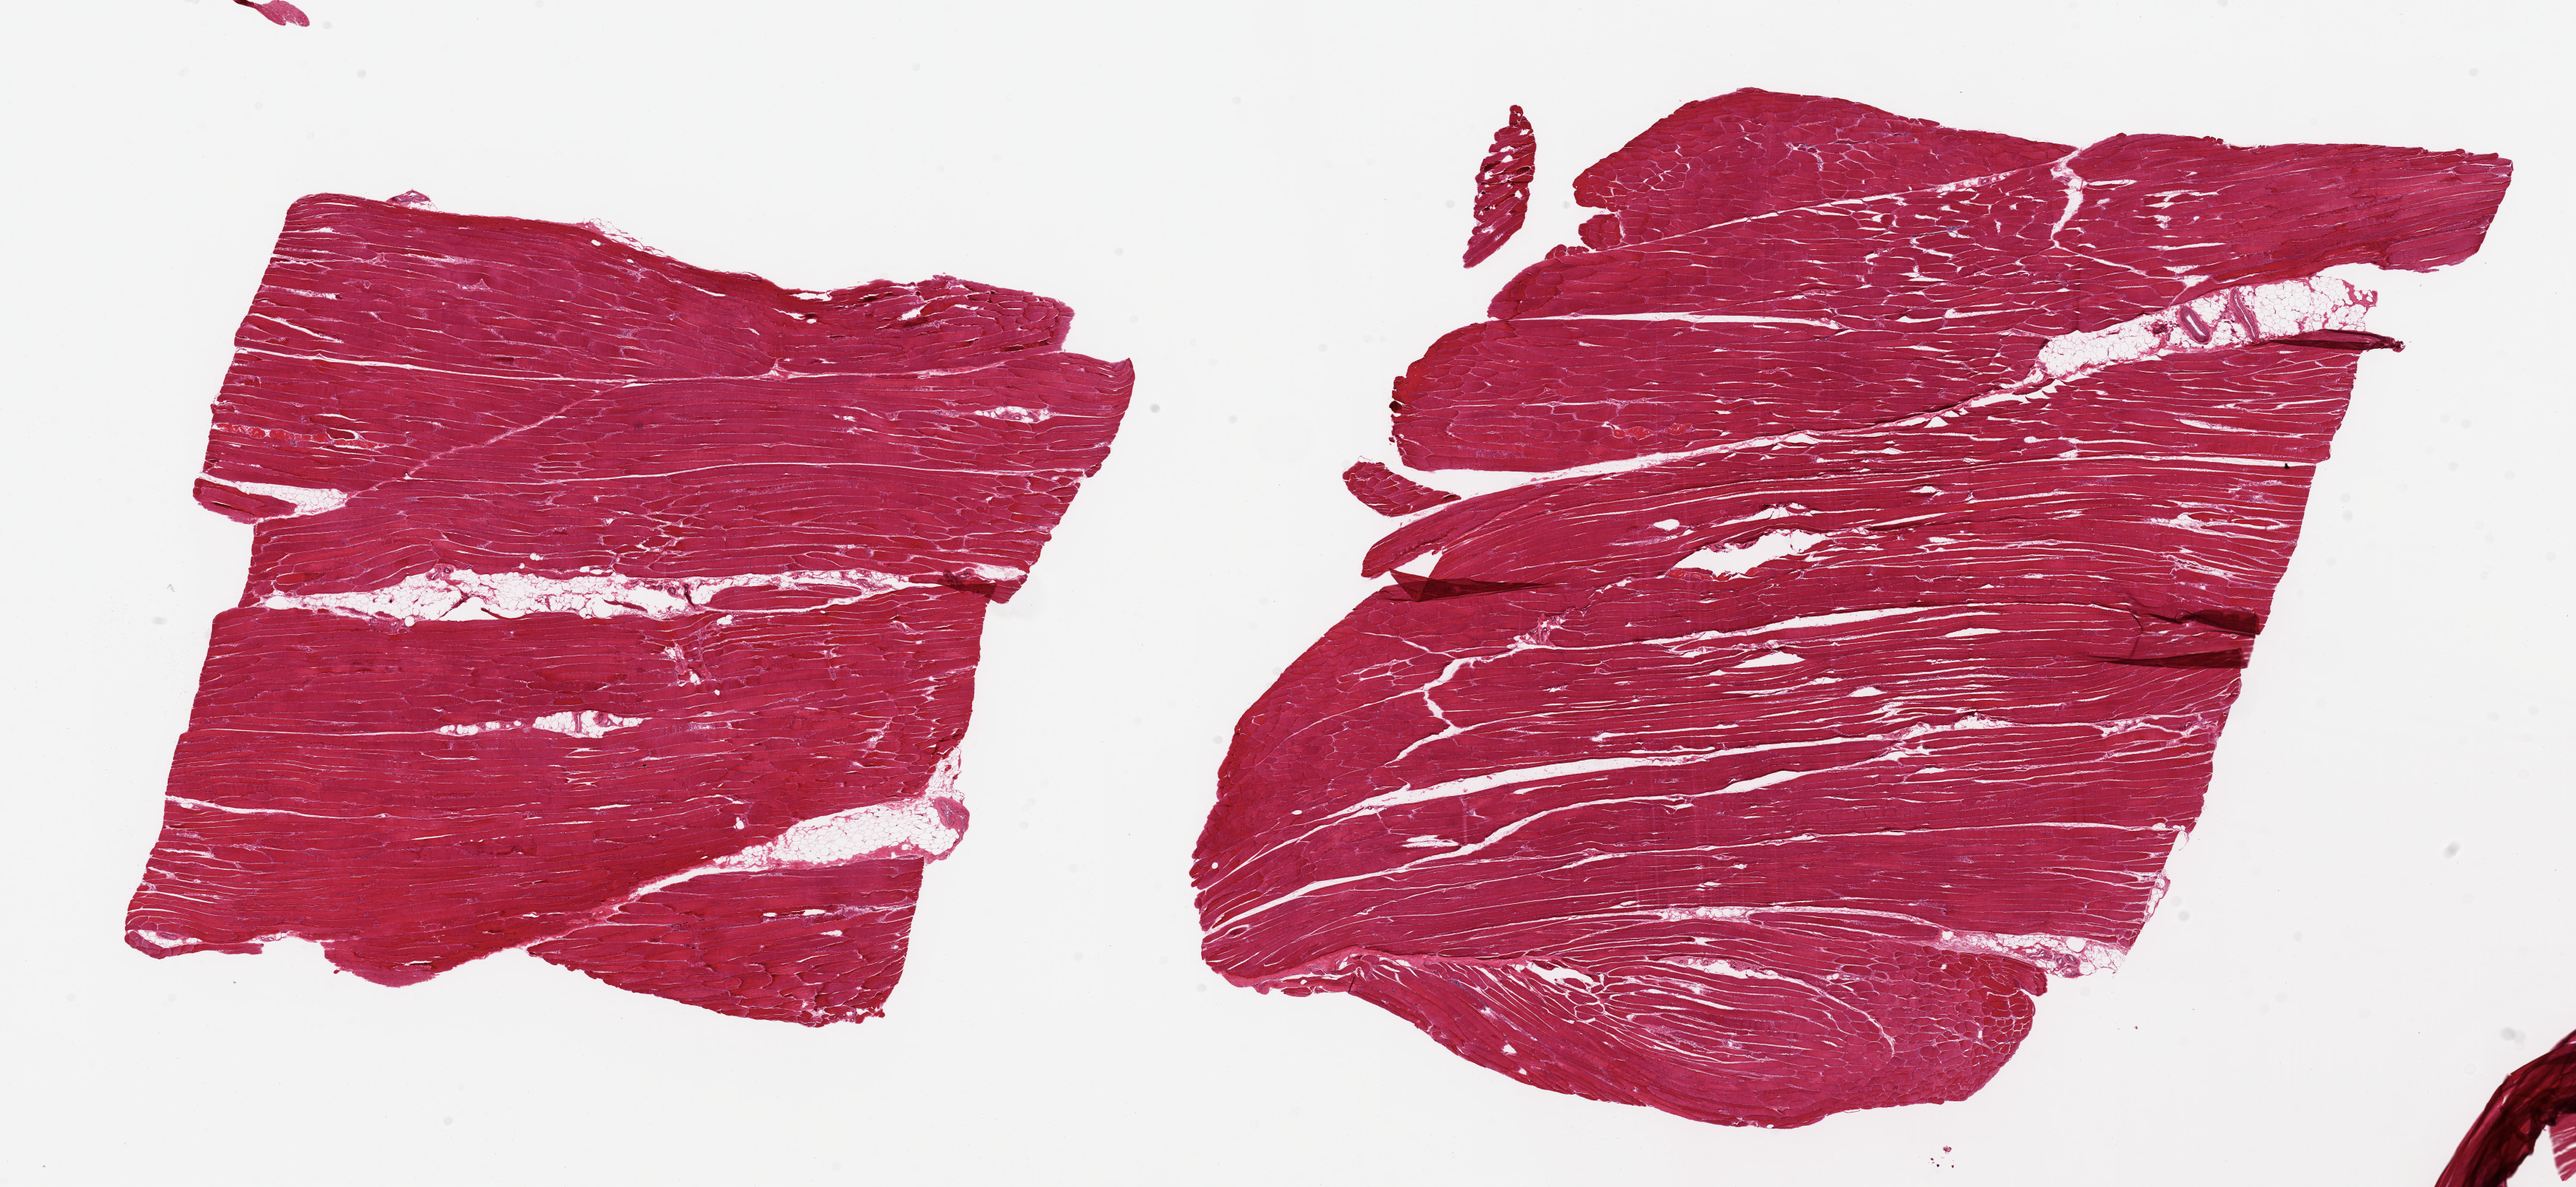
Digitized H&E-stained section, brightfield, a low-resolution overview of the entire scanned area, about 27.6 x 12.7 mm (from a 20x scan). PAXgene-fixed, paraffin-embedded tissue. Sampled site (target tissue): skeletal muscle. Tissue donor sample.
Pathologist's review note for this sample: 2 pieces; 10% internal fat in 1 piece.